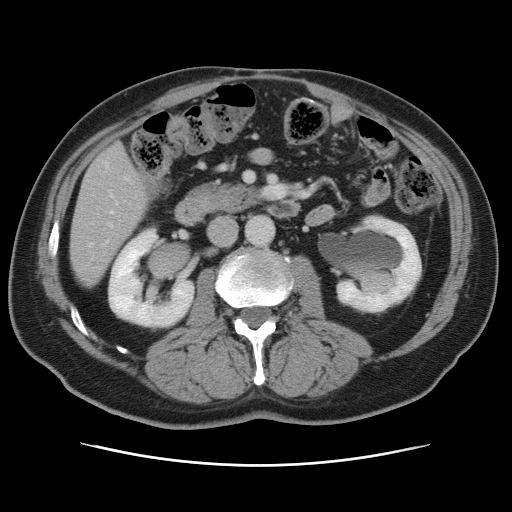
Contrast-enhanced abdominal CT, one axial slice. Slice 25 of 80 in the series (ordered by position). 120 kVp. Intravenous contrast given. Soft-tissue window (W 400 / L 40 HU). 5 mm slice thickness. 512 × 512 image matrix, field of view 370 × 370 mm. Male patient, age 69 years. From the clinical record (not read from this slice): diagnosis: colorectal cancer liver metastases, imaged before liver resection.
Structures marked on this image (expert manual segmentation):
- hepatic veins: box from (x=88, y=164) to (x=117, y=247) px
- liver: (x=71, y=146)–(x=148, y=287)
- planned liver remnant (the part of the liver to remain after resection): (x=71, y=220)–(x=128, y=287)